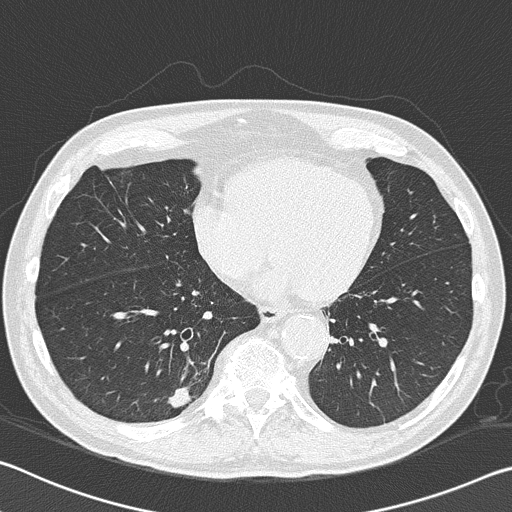
Low-dose screening chest CT, axial slice. First (baseline) screen. Lung window (W 1500 / L -600 HU). 2 mm slice thickness. 120 kVp. Slice 115 of 168 in the series. 512 × 512 image matrix, field of view 340 × 340 mm. Male participant, aged 74 years at enrolment. Current smoker at enrolment.
Lesion marked by an expert reader, box from (x=148, y=368) to (x=213, y=428) px. The exam's reader record, not a measurement of the box and not confirmed to be the same lesion: non-calcified nodule or mass ≥4 mm, right lower lobe, 13 × 11 mm, spiculated (stellate) margins, soft tissue attenuation. Official screen result: positive, change unspecified: nodule(s) >= 4 mm or enlarging nodule(s), mass(es), or other non-specific abnormalities suspicious for lung cancer. Participant outcome: lung cancer diagnosed 414 days after this screen — bronchiolo-alveolar adenocarcinoma, NOS, right lower lobe, moderately differentiated (G2), stage IA (AJCC 6th edition), 16 mm at pathology.